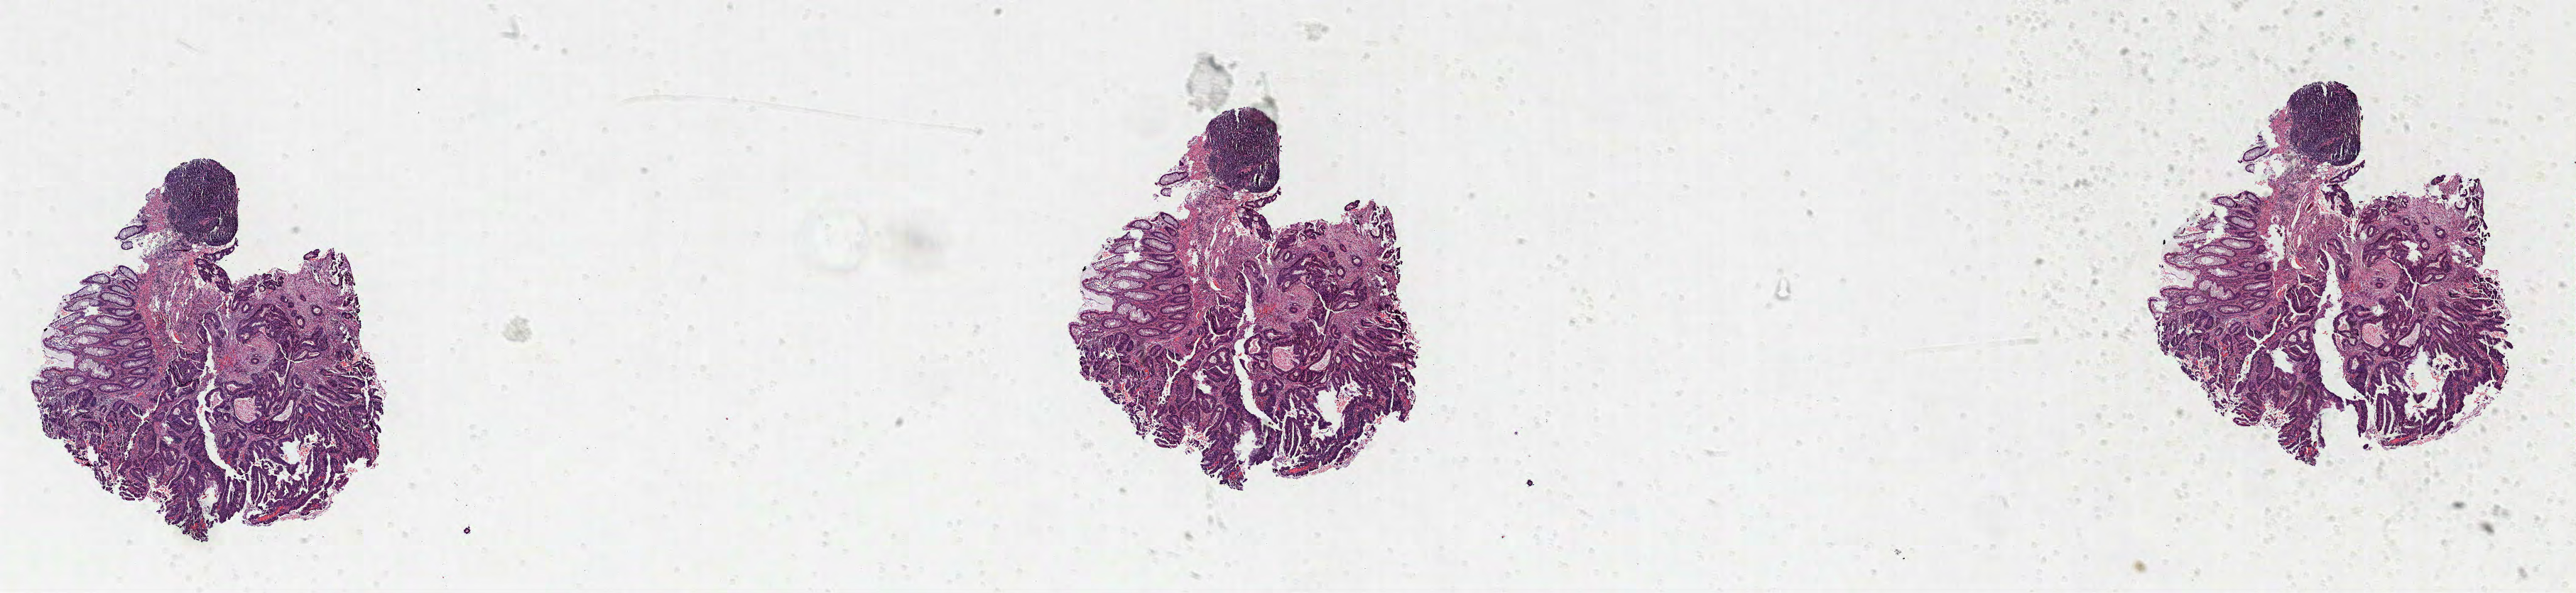
Digitized Hematoxylin and eosin (H&E) stained tissue section (whole slide) — whole scanned area (about 29.2 x 6.7 mm, acquisition: 40x scan) shown as a low-resolution overview; FFPE section; colon, primary tumour sample. Patient: male, age at initial diagnosis 56 years.
Lymph nodes positive (case pathology): 0 of 21 examined. AJCC pathologic stage: IVA (7th edition). Pathologic diagnosis: Adenocarcinoma, NOS (descending colon).